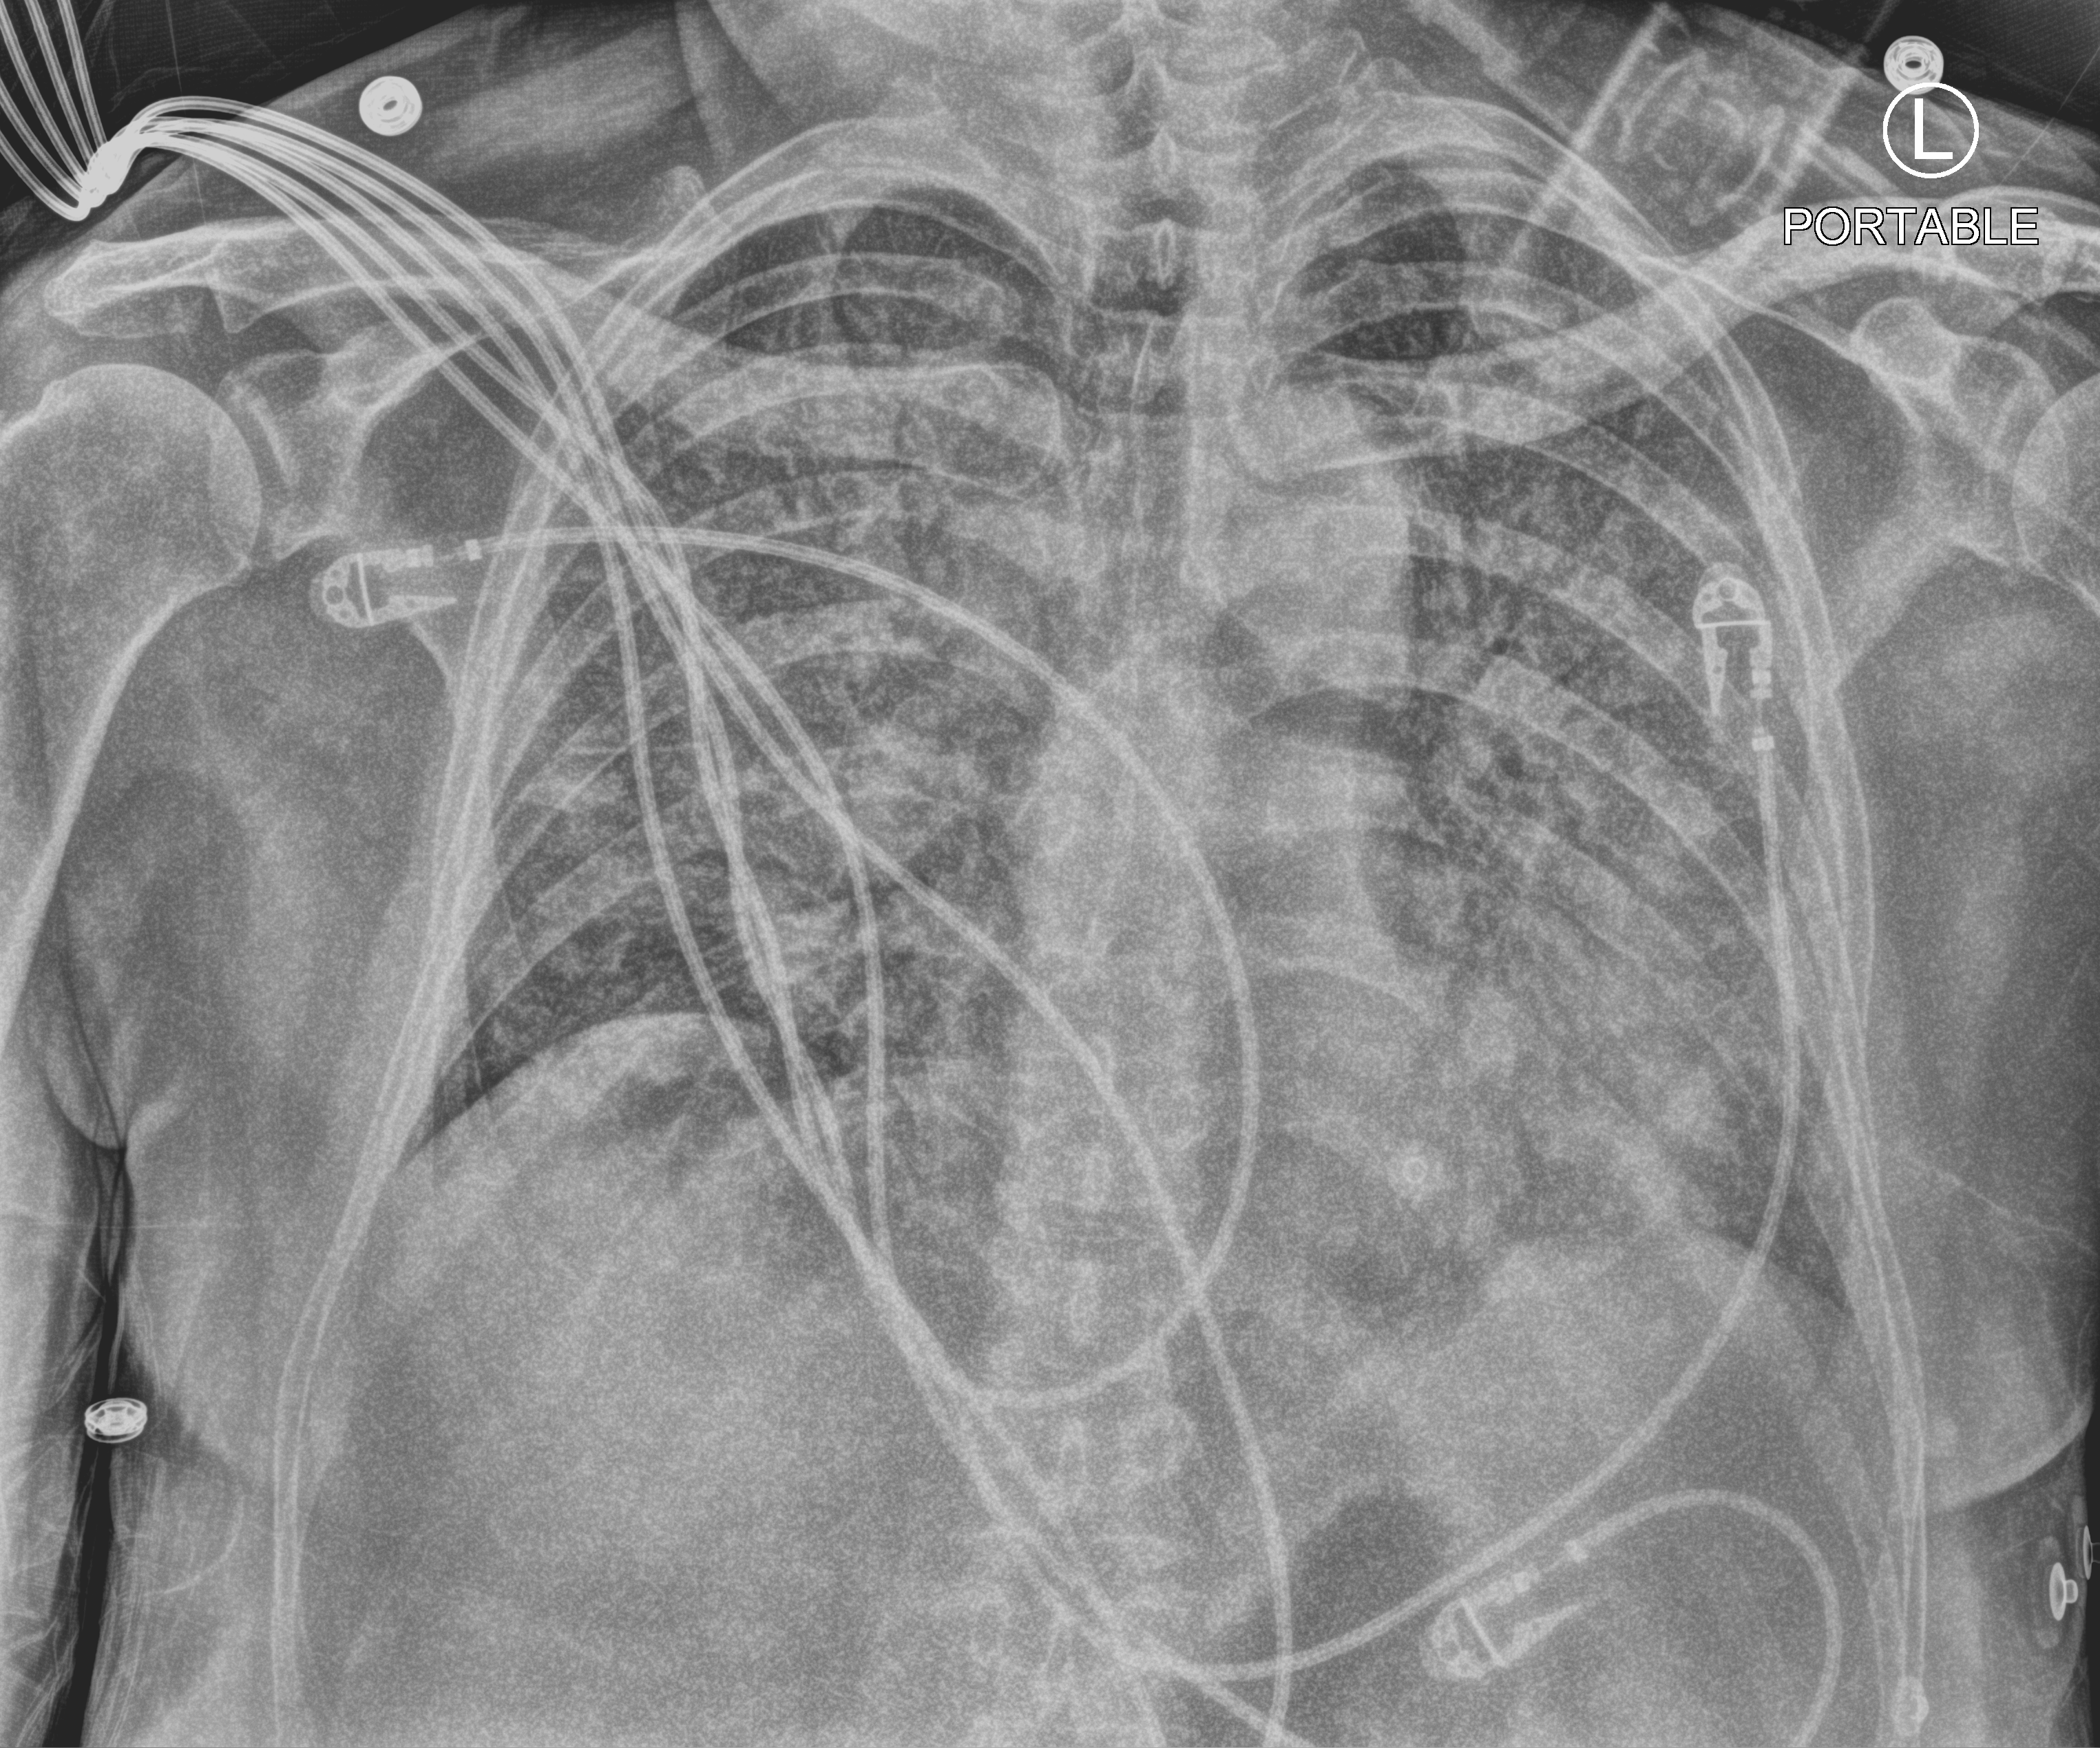
Chest X-ray (portable), anteroposterior (AP) projection. Male patient hospitalised with COVID-19, age 60–74 years.
From the hospital-stay record, not from the radiograph (when in the stay this image was taken is not recorded): COPD (admission record): no.